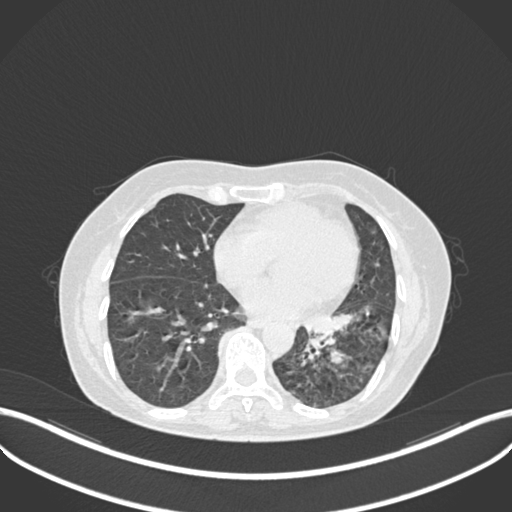
Chest CT, one axial slice; slice 103 of 270 in the series (ordered by position); reconstruction kernel B30f; 120 kVp; lung window (W 1500 / L -600 HU); 1 mm slice thickness; 512 × 512 image matrix. Female patient, age 63 years. From the clinical record (not read from this slice): clinical TNM (as recorded): T1b N0 M0; histopathological grade: G2-3.
Structures marked on this image (bounding box drawn by a radiologist):
- lung tumour (recorded histology: adenocarcinoma): bounding box (x1, y1, x2, y2) in pixels: (300, 307, 359, 337)